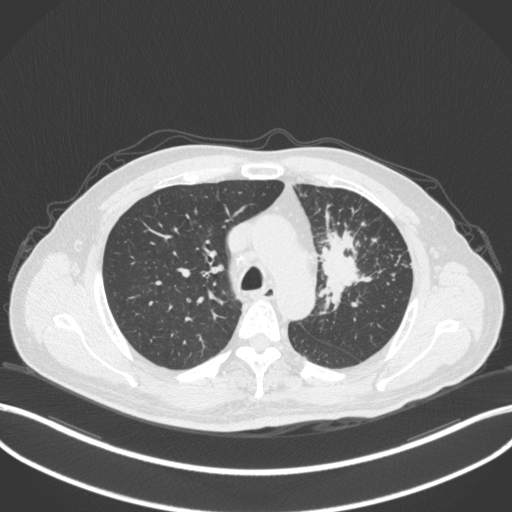
Chest CT, one axial slice. Slice 249 of 386 in the series (ordered by position). Reconstruction kernel B31f. 120 kVp. Lung window (W 1500 / L -600 HU). 1 mm slice thickness. 512 × 512 image matrix, field of view 400 × 400 mm. Patient: male, 69 years. Case-level facts recorded for this patient, not image findings: clinical TNM (as recorded): T2a N2 M0; histopathological grade: G2-3.
Structures marked on this image (bounding box drawn by a radiologist):
- lung tumour (recorded histology: adenocarcinoma): bounding box (x1, y1, x2, y2) in pixels: (315, 223, 379, 318)